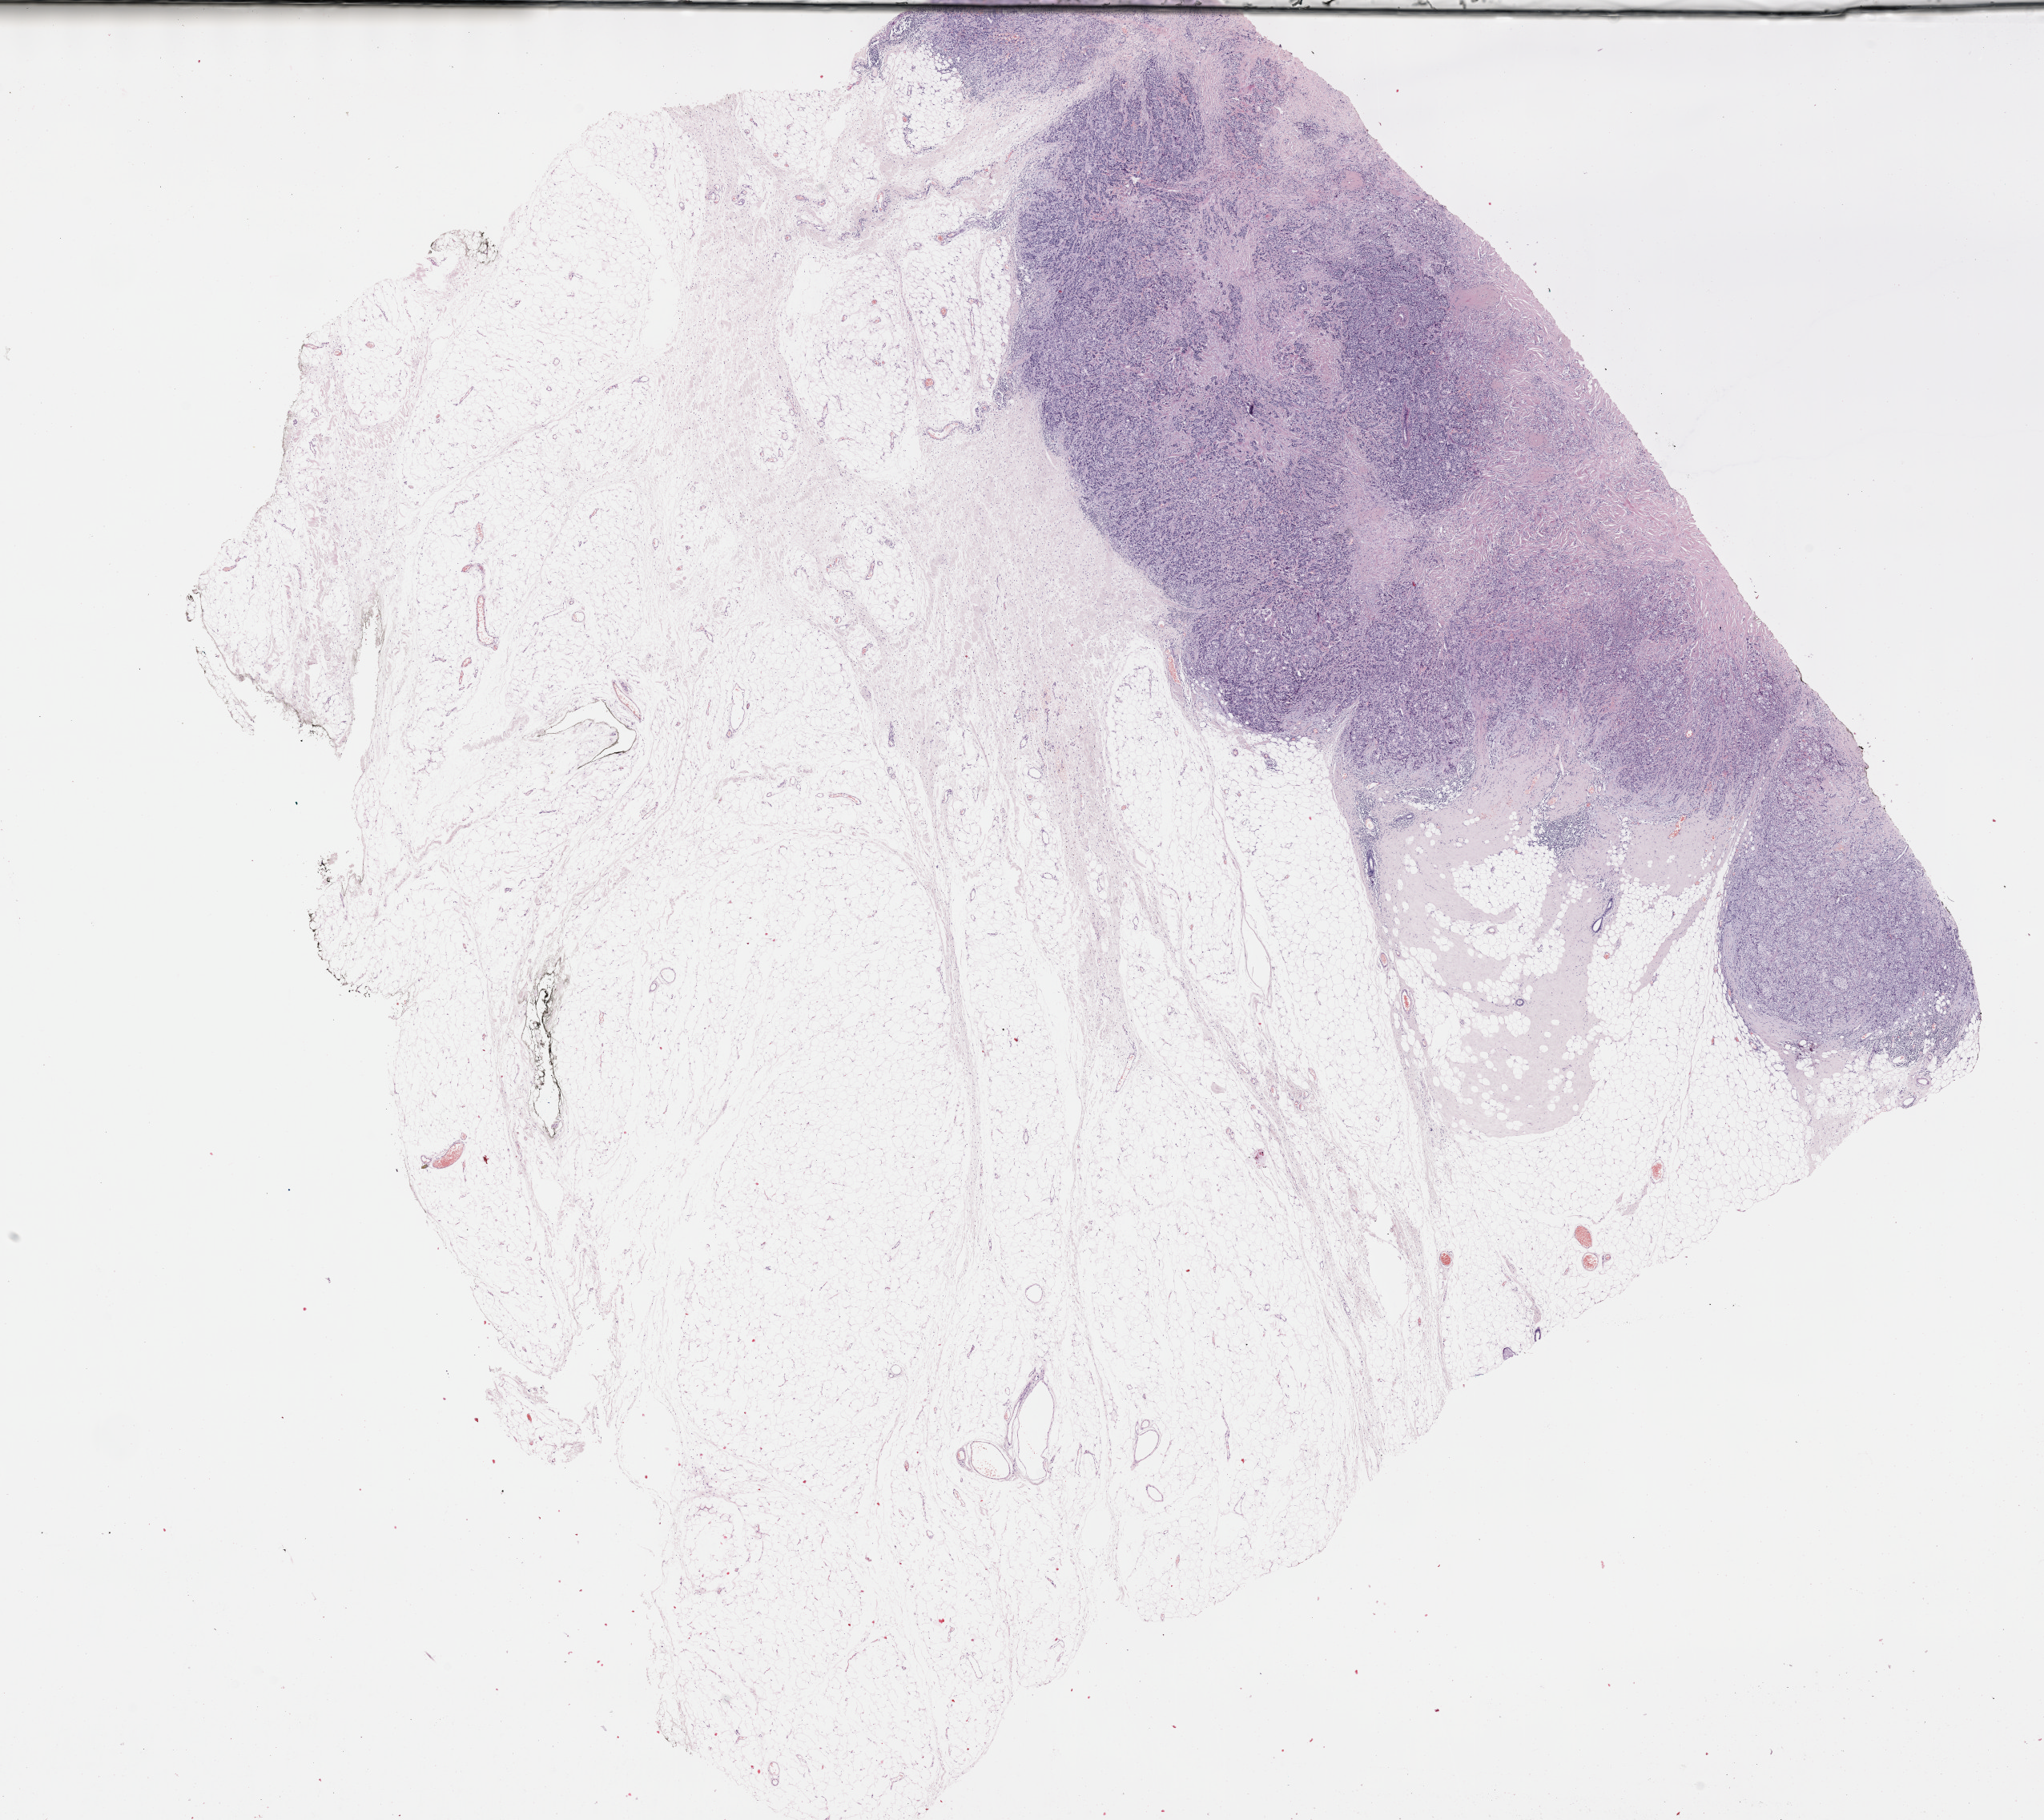
Digitized Hematoxylin and eosin (H&E) stained tissue section (whole slide), whole scanned area (about 20.6 x 18.4 mm, slide scanned at 40x) shown as a low-resolution overview. Formalin-fixed paraffin-embedded (FFPE) diagnostic section. Breast, primary tumour sample. Female patient; age at initial diagnosis 62 years.
Laterality: left. AJCC pathologic stage: IIB. Pathologic diagnosis: Infiltrating duct carcinoma, NOS.